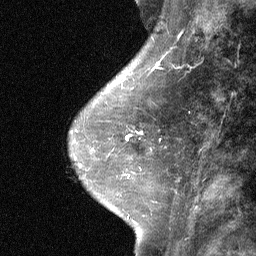
Breast MRI (dynamic contrast-enhanced), one sagittal slice; dynamic contrast-enhanced study with each time point stored as its own series, time point 2 of 3 at this slice position (early post-contrast, ordered by acquisition time); 1.5 T; TE 4.8 ms, TR 27 ms; 2 mm slice thickness; 256 × 256 image matrix. Patient: female, 42 years. From the clinical record (not read from this slice): setting: breast cancer imaged before/during neoadjuvant chemotherapy; receptor status: triple-negative.
Outlined on this slice (semi-automatically segmented with operator editing):
- analysis volume of interest (the breast-tissue region the enhancement analysis was run in; not a lesion): bounding box (x1, y1, x2, y2) in pixels: (99, 117, 167, 187)
- tumour enhancement mask (voxels above the 90 % enhancement threshold inside the analysis volume of interest): (126, 133, 142, 140)